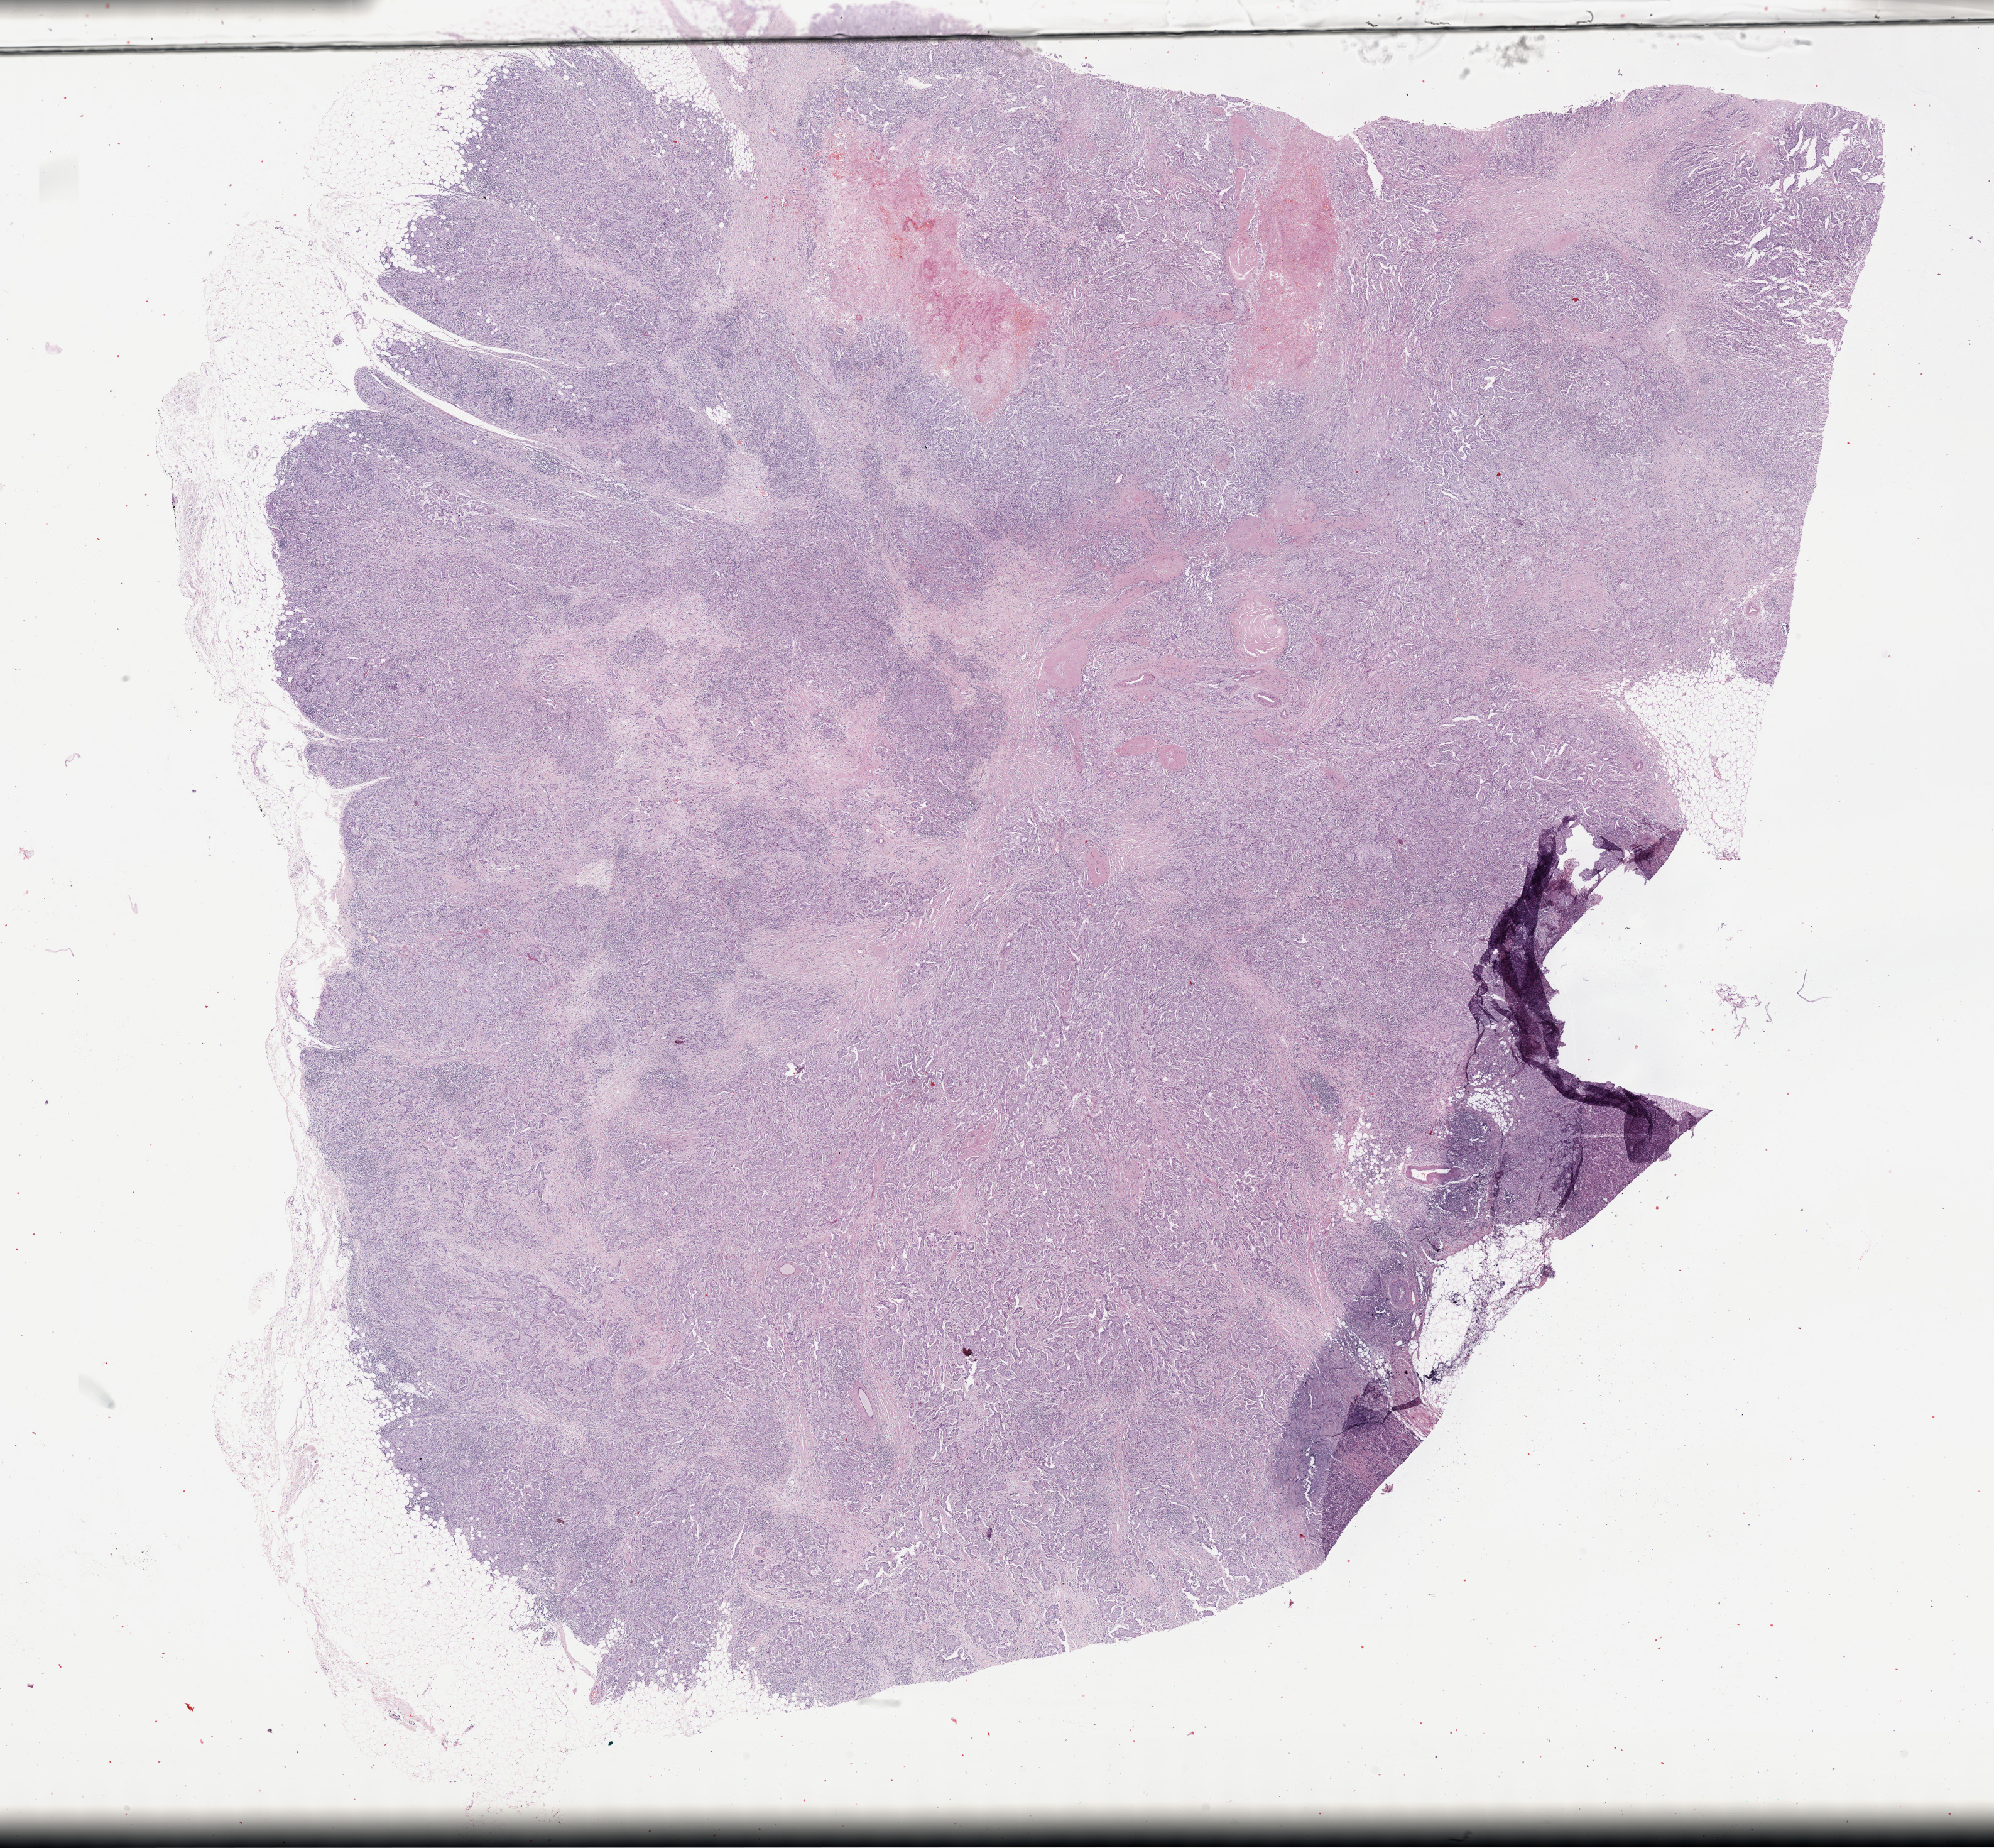
Digitized H&E-stained tissue section (whole slide), shown as a low-resolution overview of the whole scanned area (about 25.7 x 23.8 mm), formalin-fixed paraffin-embedded (FFPE) diagnostic section, sample: primary tumour, breast. Female patient; age at initial diagnosis 77 years.
AJCC pathologic stage: IIB (7th edition). Laterality: right. Diagnosis: Infiltrating duct carcinoma, NOS. Lymph nodes positive (case pathology): 3 of 16 examined. TNM: T2 N1a M0.